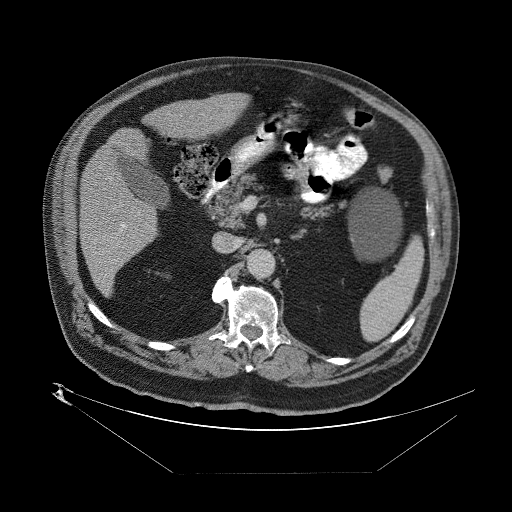
Contrast-enhanced abdominal CT (liver protocol), one axial slice; position 33 of 89 along the scan axis; reconstruction kernel STANDARD; one of 2 acquisitions stored at this slice position; soft-tissue window (W 400 / L 40 HU); 2.5 mm slice thickness; 512 × 512 image matrix, field of view 480 × 480 mm. From the clinical record (not read from this slice): diagnosis: hepatocellular carcinoma (patient treated with transarterial chemoembolisation; whether this scan precedes or follows treatment is not stated here); TNM stage (as recorded): Stage-II; Child-Pugh class: B; tumour differentiation: moderately differentiated; tumour nodularity: multinodular.
Annotated regions visible in this slice (semi-automatically segmented with operator editing):
- abdominal aorta: bounding box (x1, y1, x2, y2) in pixels: (248, 251, 273, 277)
- liver parenchyma outside the tumour (the mass and vessels are separate outlines, so this box may not span the whole liver): (78, 92, 244, 298)
- liver vessels: (96, 211, 139, 264)